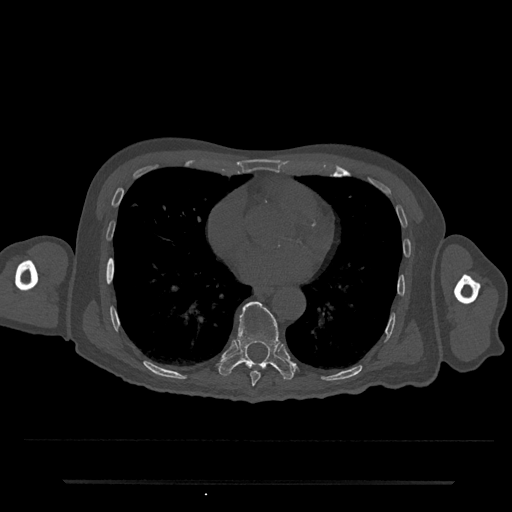
CT including the spine, one axial slice; position 385 of 797 along the scan axis; bone window (W 1800 / L 400 HU); 512 × 512 image matrix, field of view 427 × 427 mm. Male patient, age 74 years. From the clinical record (not read from this slice): primary cancer: prostate.
Structures marked on this image (semi-automatically segmented with operator editing):
- T8 vertebra: bounding box <250,371,261,386> (left, top, right, bottom; pixels)
- T9 vertebra: <219,301,295,380>